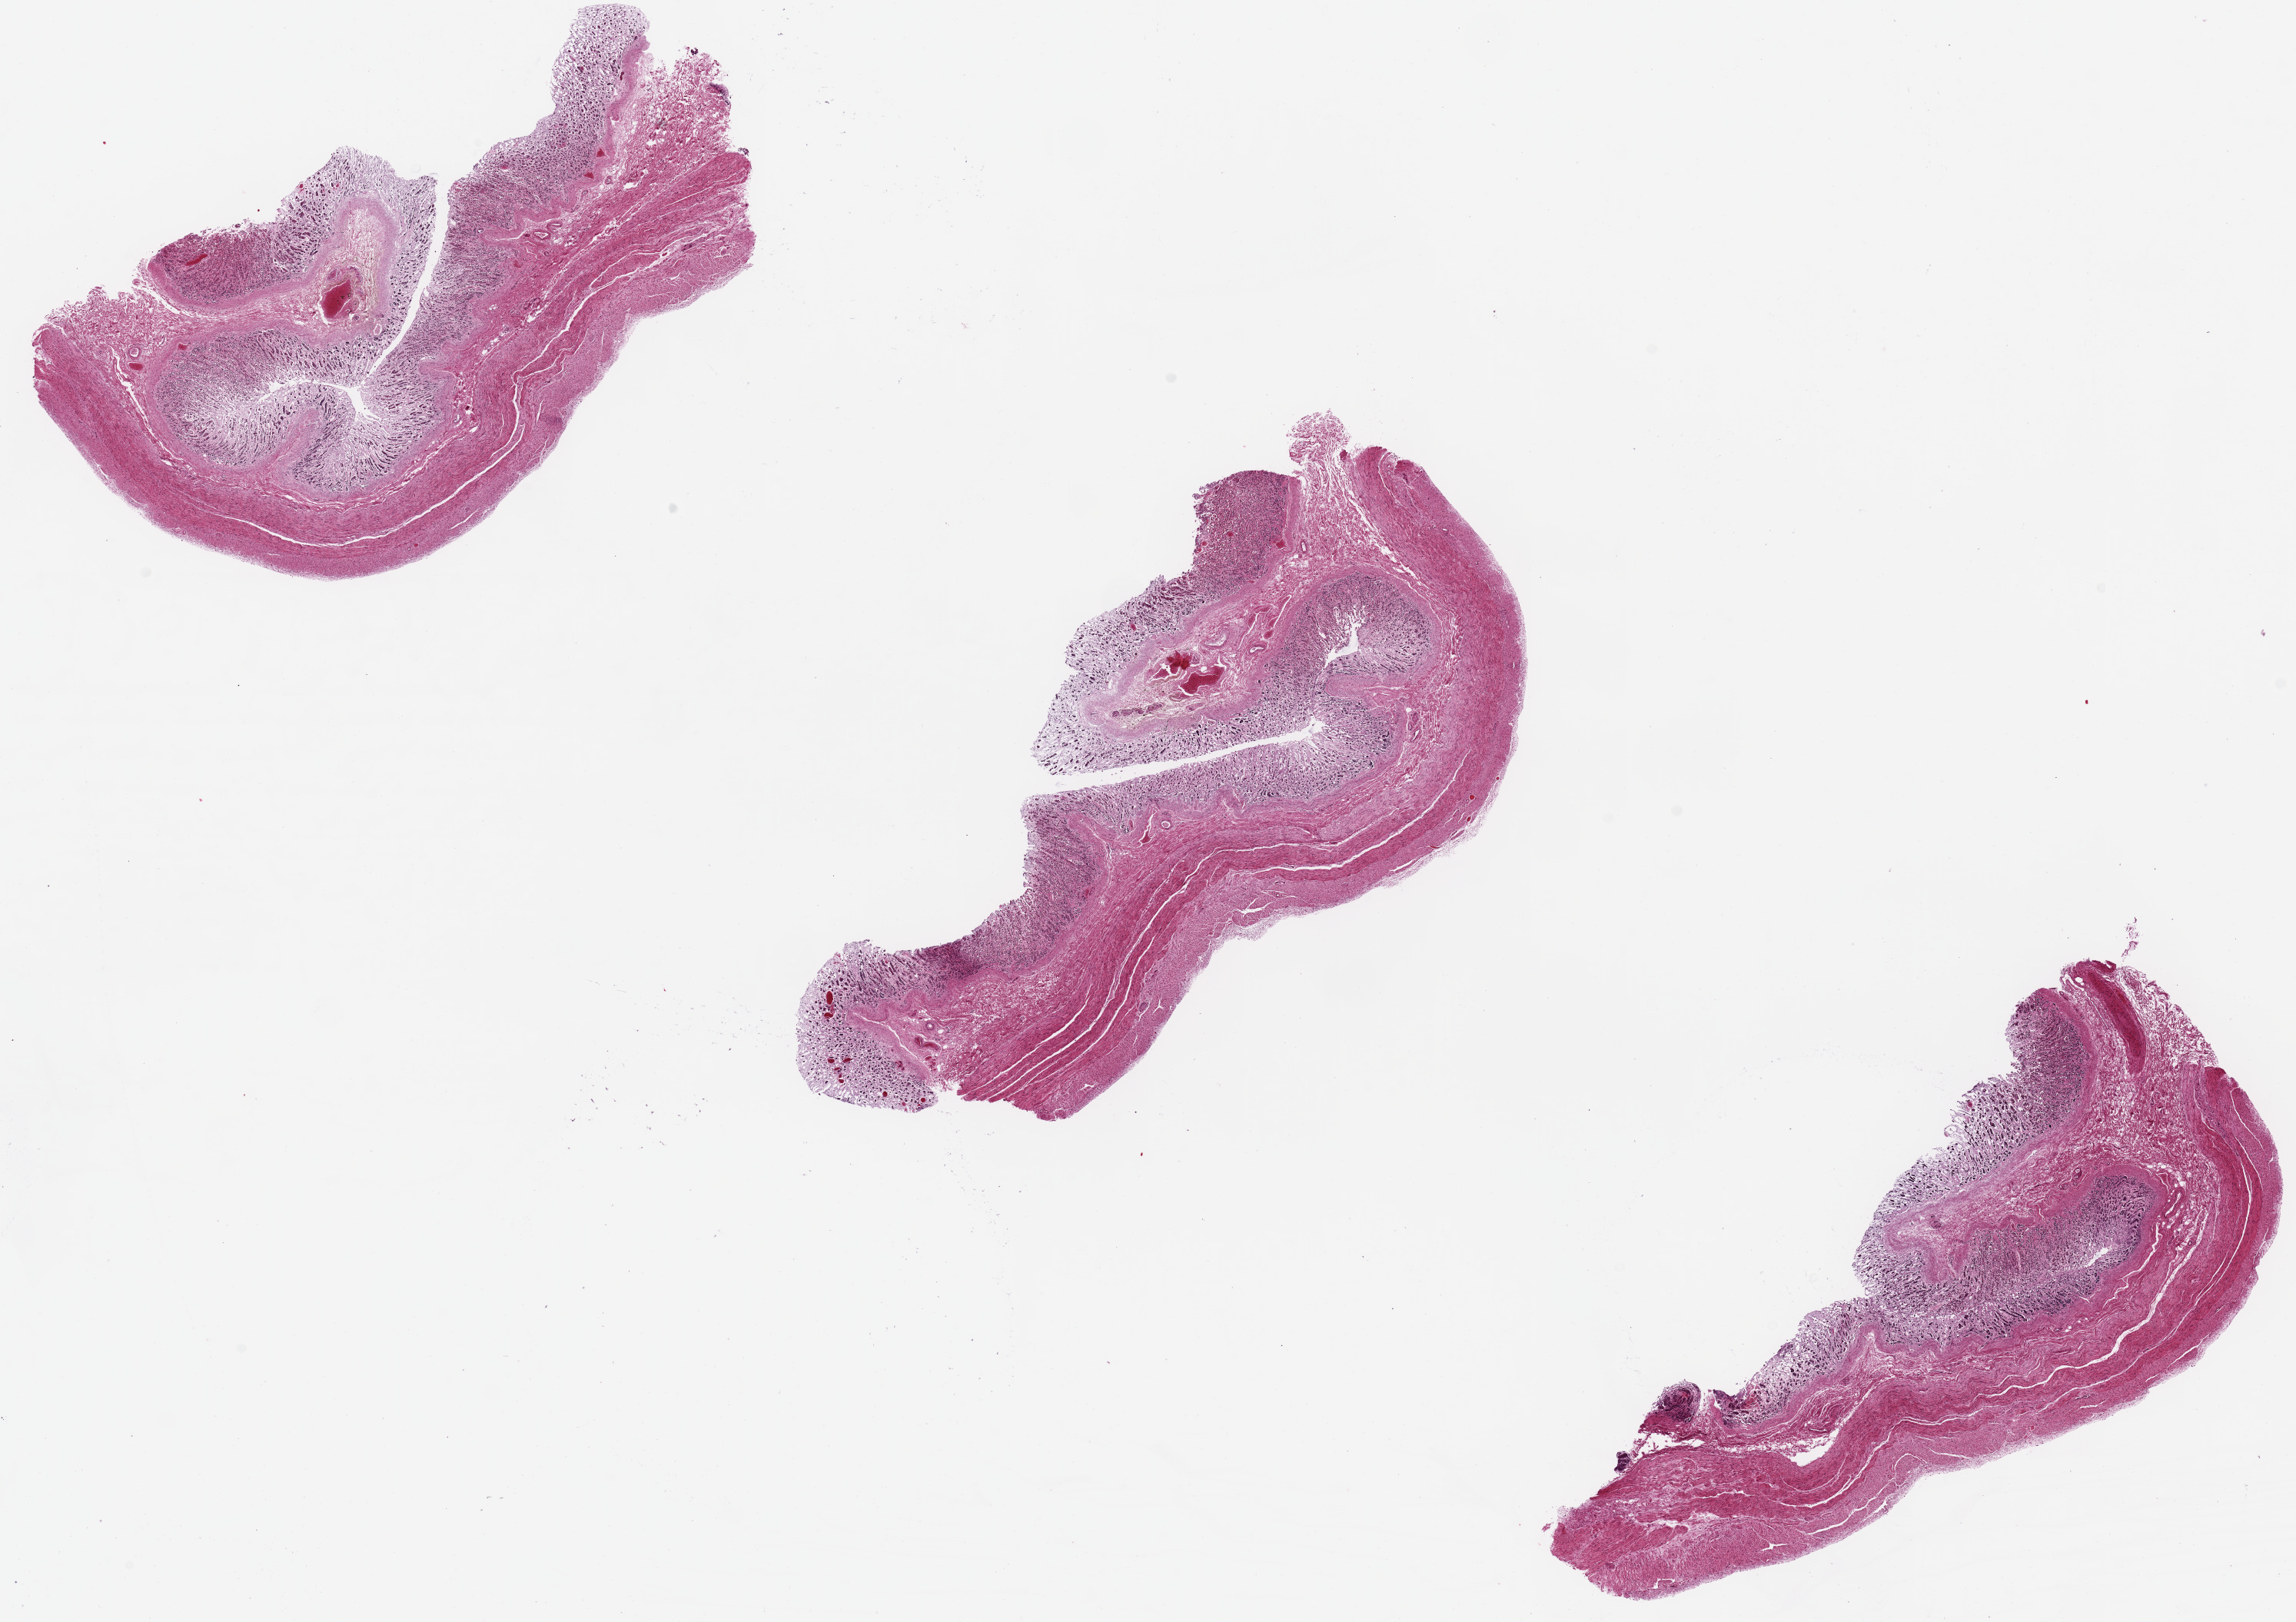
H&E whole-slide image, brightfield — low-resolution overview of the scanned area, about 23.6 x 16.7 mm (slide scanned at 20x). PAXgene-fixed paraffin-embedded (PFPE) section. Section of stomach (target tissue). Tissue donor sample.
Review note (as recorded): Epithelium 100% autolyzed (???Score 3???).